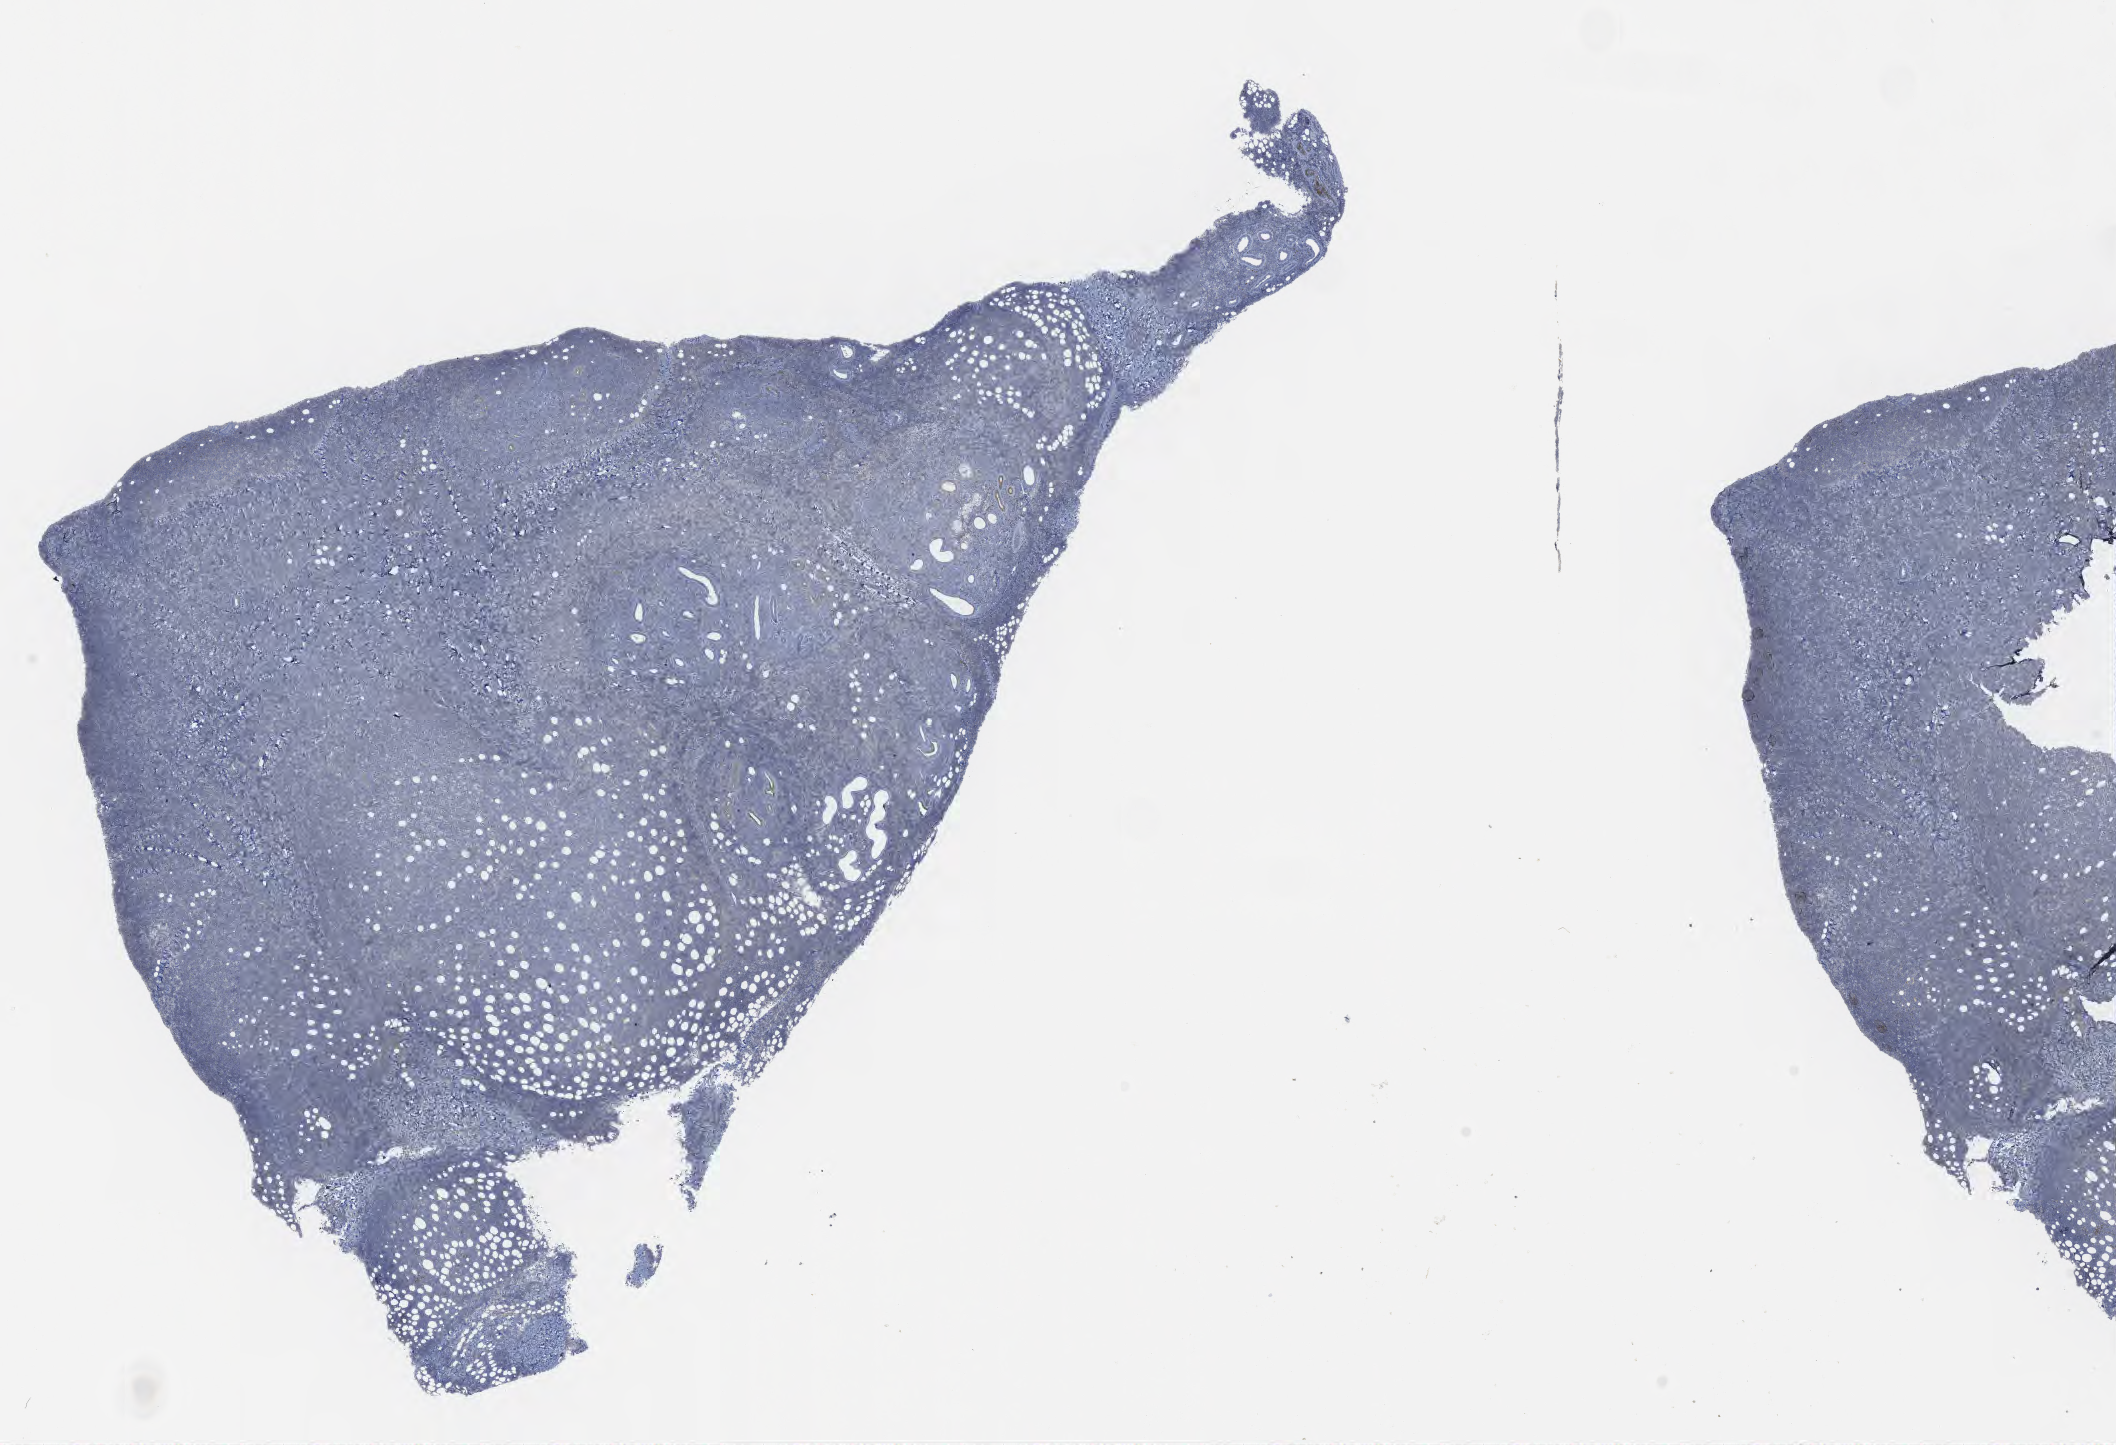
IHC for BCL2, whole-slide image, a low-resolution overview of the entire scanned area, about 17.1 x 11.7 mm; tumor tissue. Patient male; 46 years old.
Histologic diagnosis: Burkitt lymphoma, NOS.